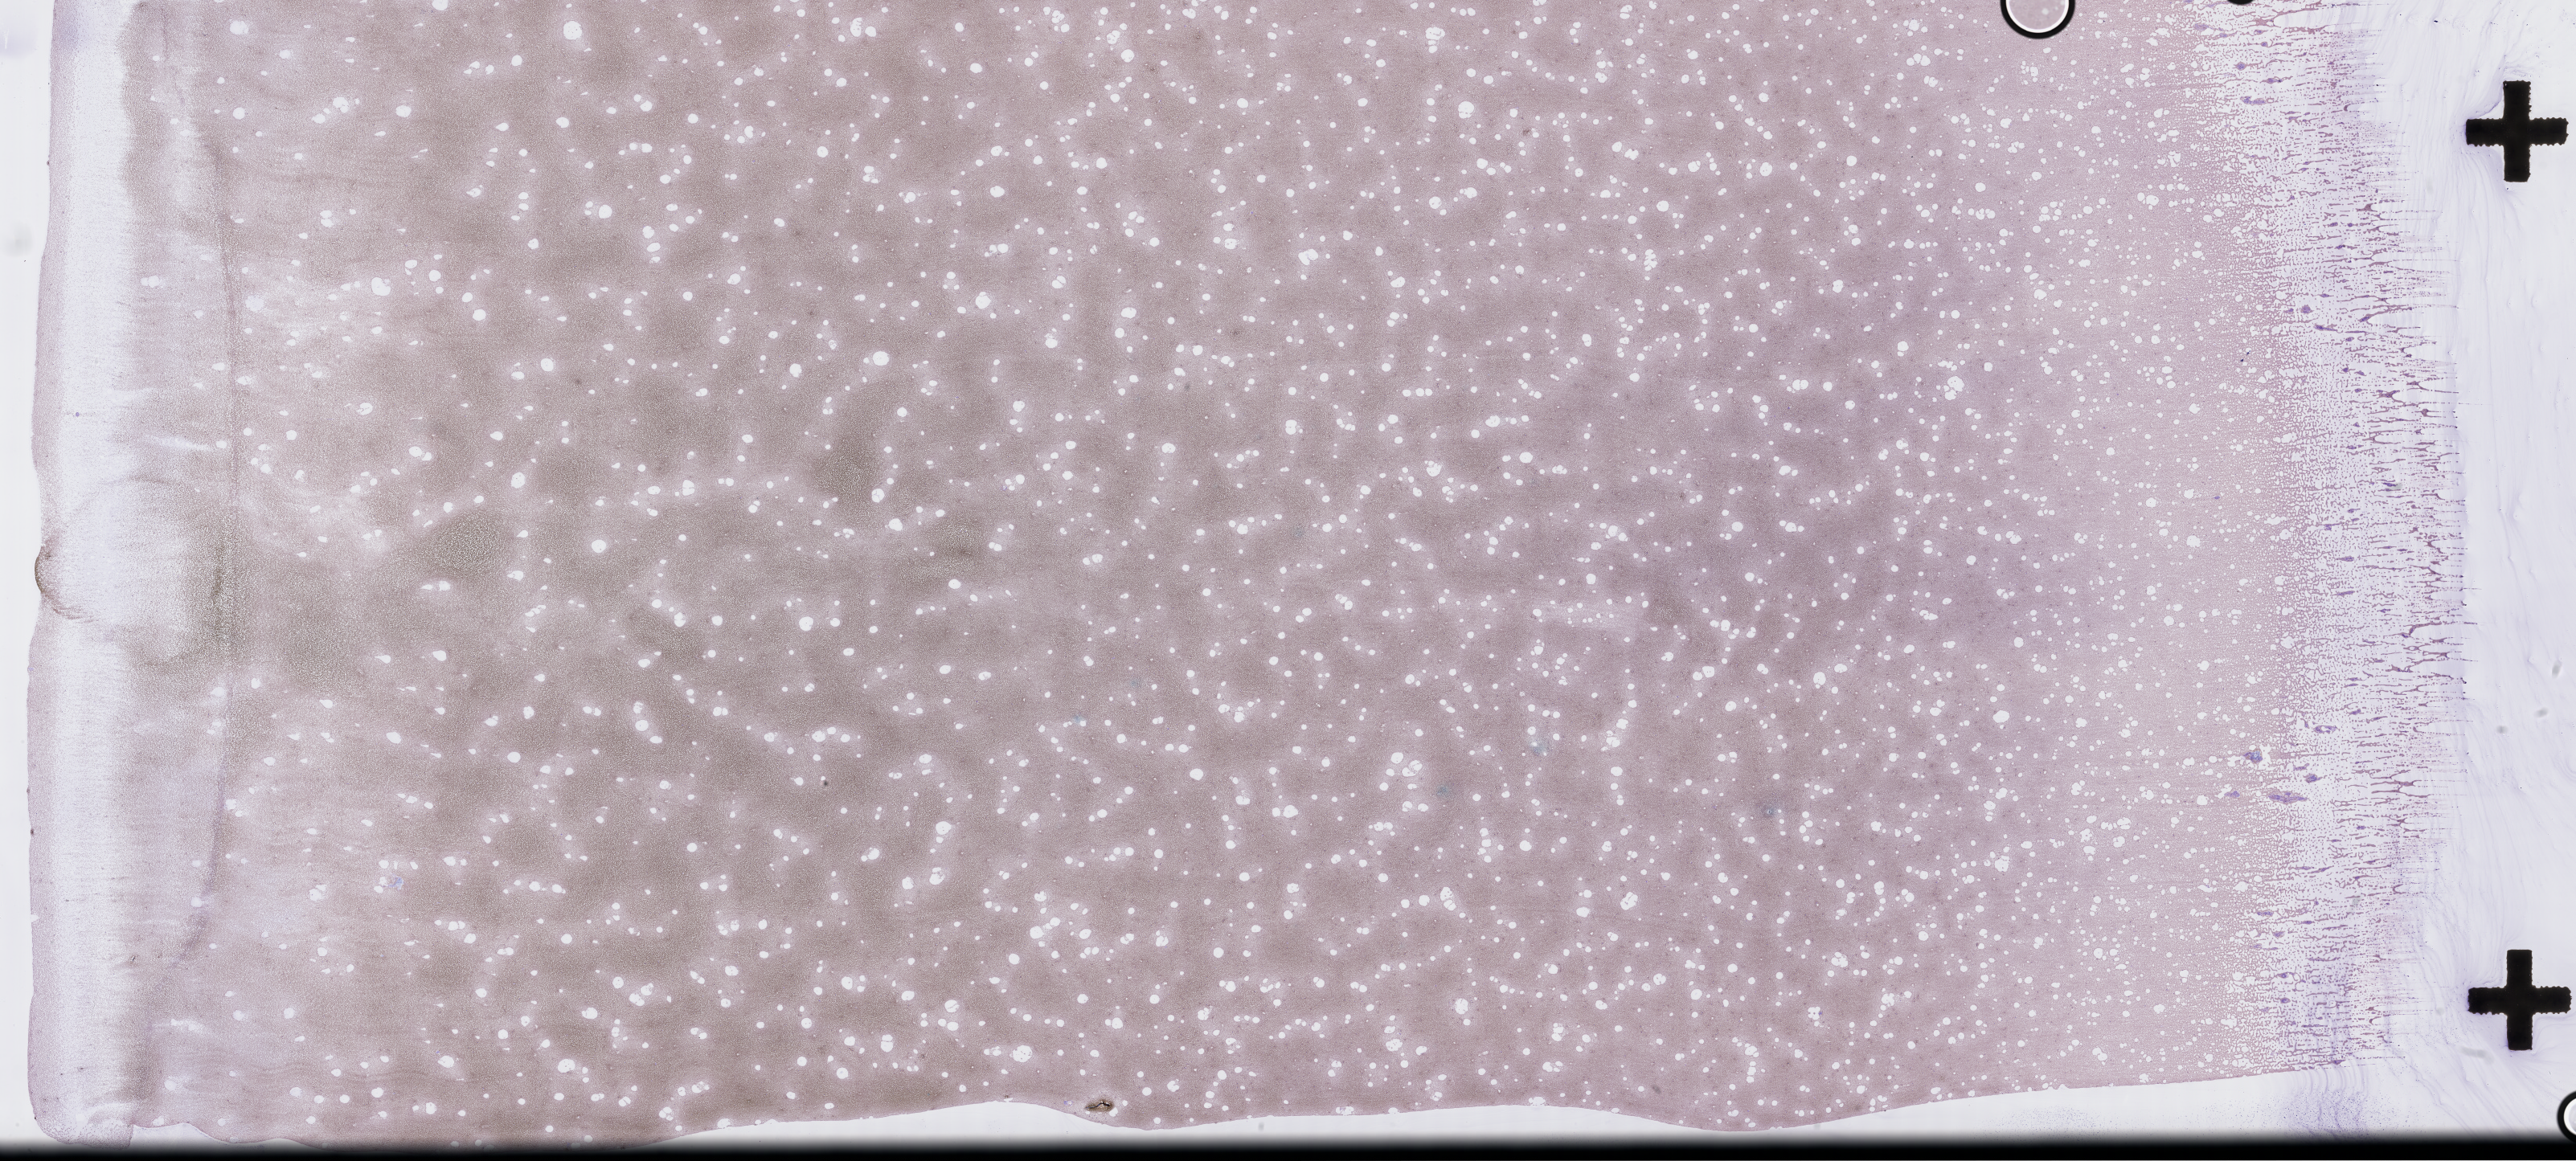
Wright-Giemsa-stained whole blood smear, whole-slide image — a low-resolution overview of the entire scanned area, about 51.8 x 23.3 mm; smear from an EDTA sample; specimen time point: collected on treatment. Patient sex: male.
• patient diagnosis: Plasma Cell Myeloma